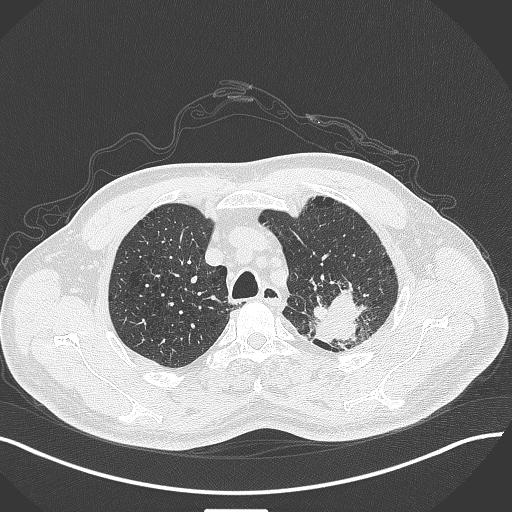
Chest CT, one axial slice; position 340 of 429 along the scan axis; 120 kVp; lung window (W 1500 / L -600 HU); 1 mm slice thickness; 512 × 512 image matrix. Patient: male, 55 years. From the clinical record (not read from this slice): clinical TNM (as recorded): T3 N0 M1c; histopathological grade: G3.
Annotated regions visible in this slice (rectangle marked by the reading radiologist):
- lung tumour (recorded histology: adenocarcinoma): box from (x=311, y=290) to (x=380, y=354) px